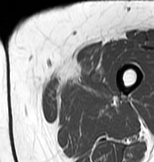
MRI of an extremity soft-tissue mass, one axial slice. Slice 7 of 83 in the series (ordered by position). MR volume resampled by the dataset authors to the PET/CT grid (not the native acquisition matrix). 3.27 mm slice thickness. 154 × 162 image matrix, field of view 150 × 158 mm. Female patient. Case-level facts recorded for this patient, not image findings: histological type: myxofibrosarcoma; grade: intermediate; site of the primary tumour: left thigh.
Annotated regions visible in this slice (expert contour drawn on MRI and transferred to this co-registered scan by the dataset authors):
- gross tumour volume including surrounding oedema: bounding box [x1, y1, x2, y2] px = [44, 61, 109, 101]